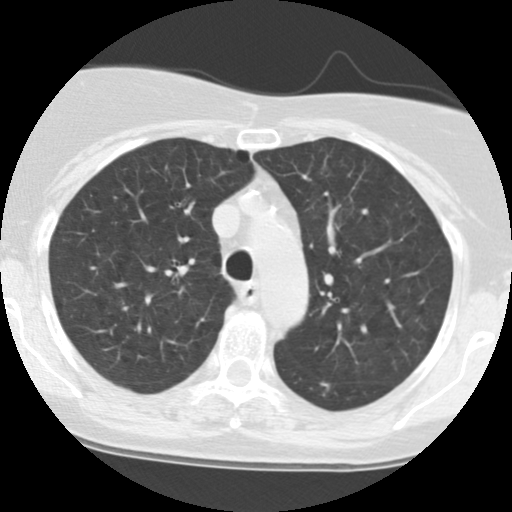
Low-dose screening chest CT, axial slice, first (baseline) screen, lung window (W 1500 / L -600 HU), standard (soft-tissue) reconstruction kernel (STANDARD), slice 33 of 123 in the series, 512 × 512 image matrix, field of view 283 × 283 mm. Female participant, aged 63 years at enrolment.
• Expert-annotated lung lesion, bounding box [x1, y1, x2, y2] px = [307, 375, 345, 409].
• The screening reader recorded 2 non-calcified nodules or masses ≥4 mm on this exam; which of them this box marks is not recorded.
• Later outcome: lung cancer diagnosed 796 days after this screen (after the third annual screen) — squamous cell carcinoma, NOS, left lower lobe, moderately differentiated (G2), stage IB (AJCC 6th edition), 15 mm at pathology.